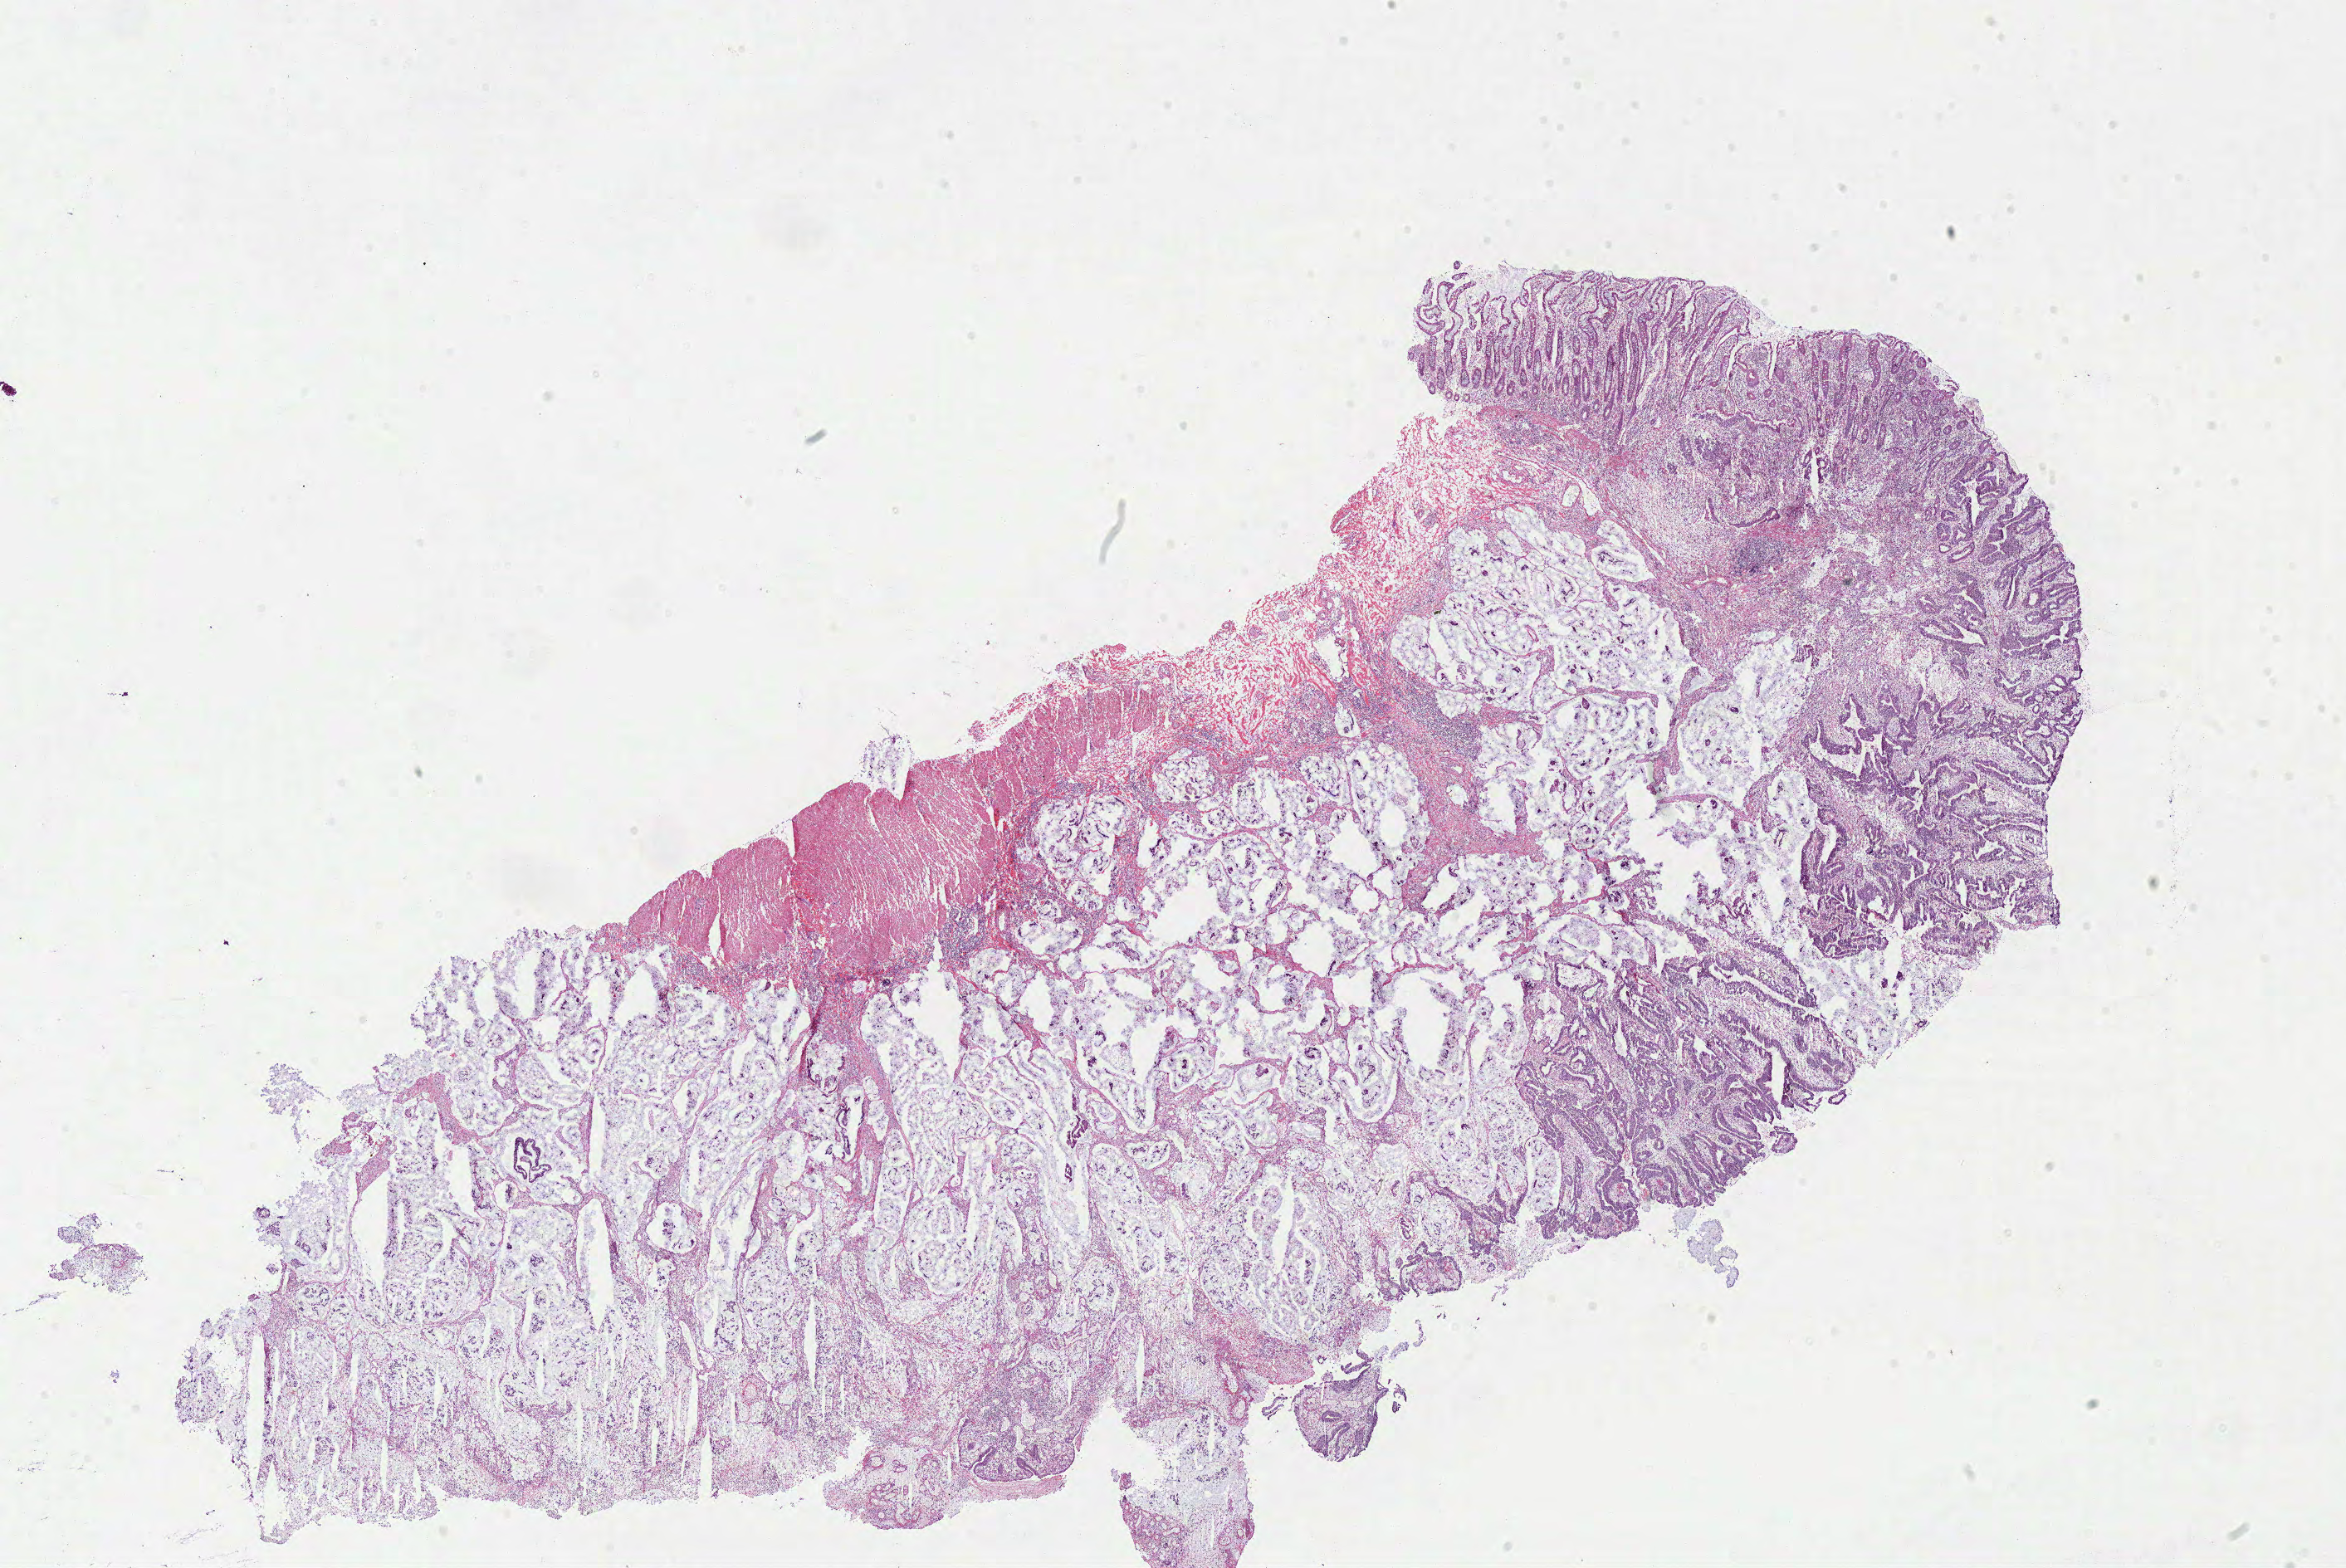
H&E whole-slide image — a low-resolution overview of the entire scanned area, about 22.3 x 14.9 mm; frozen section; colon, primary tumour sample. Female patient; age at initial diagnosis 48 years. Slide review estimates, as recorded: tumour cells 74%, tumour nuclei 77%, normal cells 10%, stromal cells 15%, necrosis 1%.
• diagnosis: Mucinous adenocarcinoma (ascending colon)
• AJCC pathologic stage: IIIB (7th edition)
• TNM: T3 N1a M0